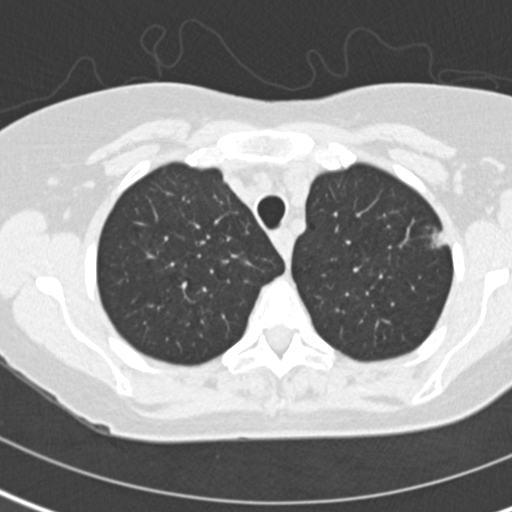
Low-dose screening chest CT, one axial slice. Reconstruction kernel B30f. 120 kVp. Lung window (W 1500 / L -600 HU). 512 × 512 image matrix, field of view 280 × 280 mm.
Structures marked on this image (manually delineated by an expert):
- lesion 1 (tumor, upper lobe of left lung): bounding box (x1, y1, x2, y2) in pixels: (432, 230, 447, 247)